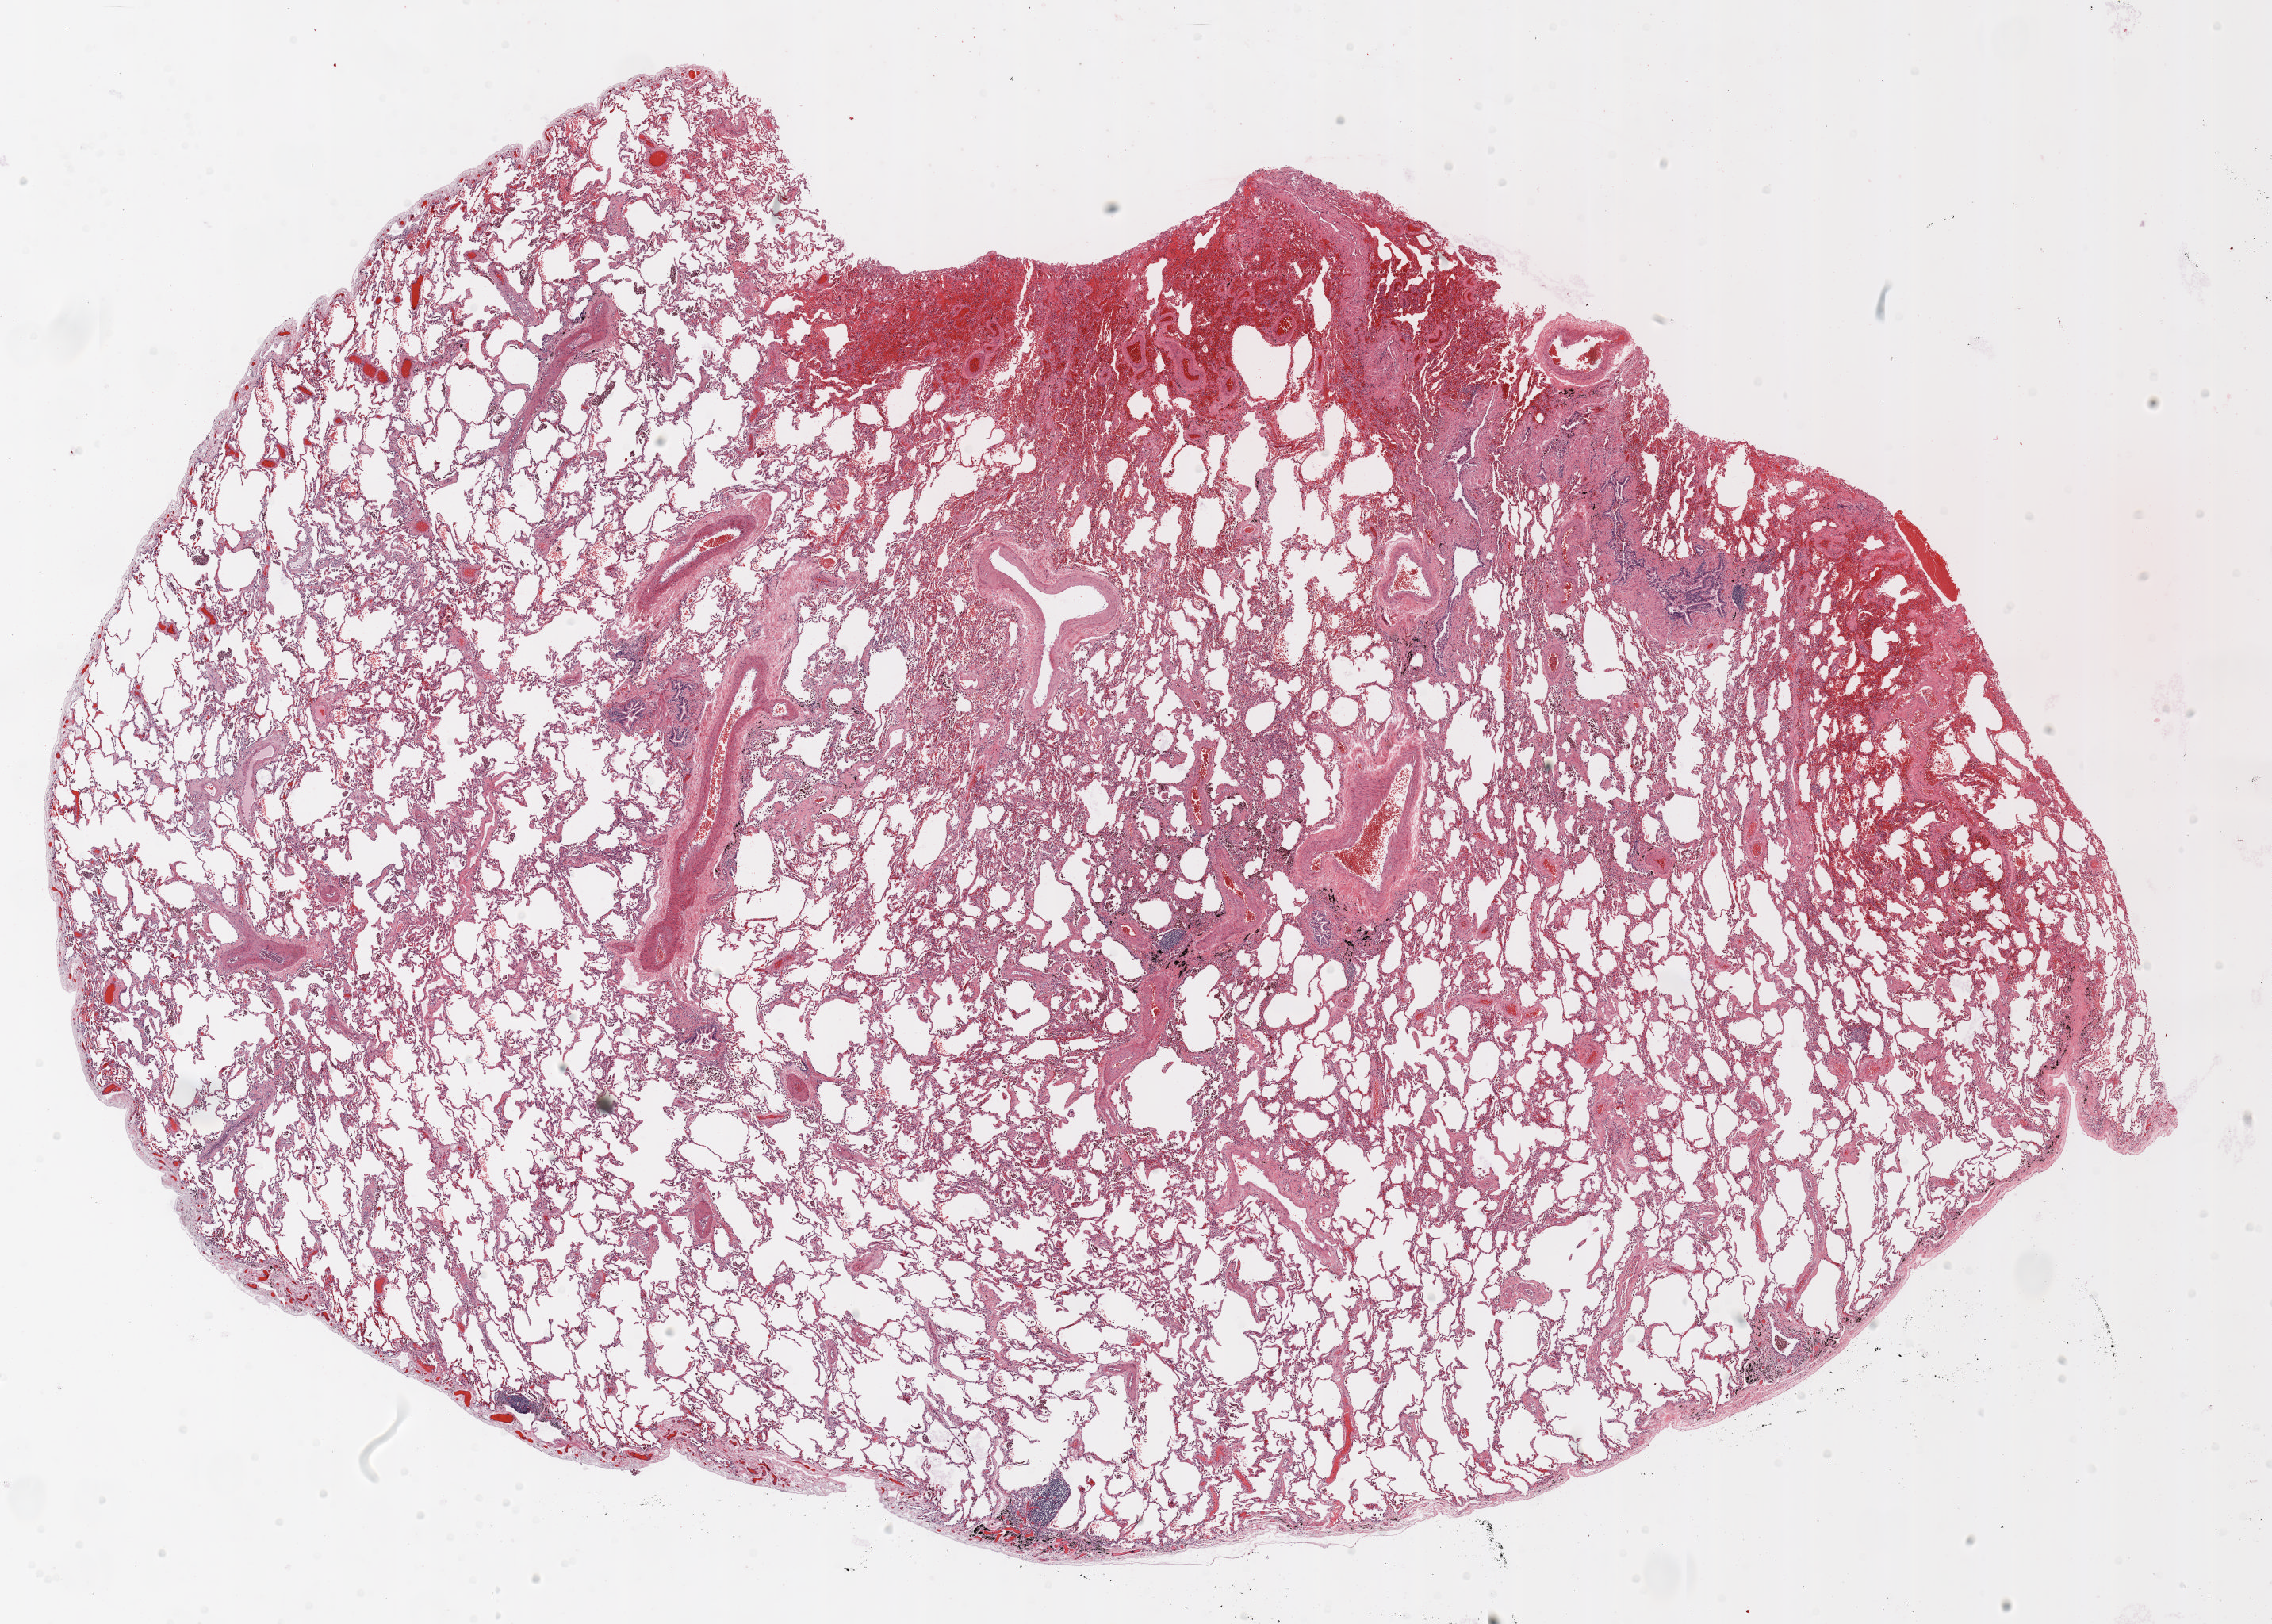
Whole-slide histology image, H&E, low-resolution overview of the scanned area, about 23.0 x 16.5 mm. FFPE section. Lung. Male, age 64 at enrolment. Current smoker at enrolment. Grade: poorly differentiated (G3).
Tumour size (pathology): 15 mm. Participant's lung-cancer diagnosis: Adenocarcinoma, NOS. Primary tumour location (clinical record): left upper lobe. Stage (AJCC 6th edition): IA. ICD-O-3 topography: upper lobe of lung (C34.1).